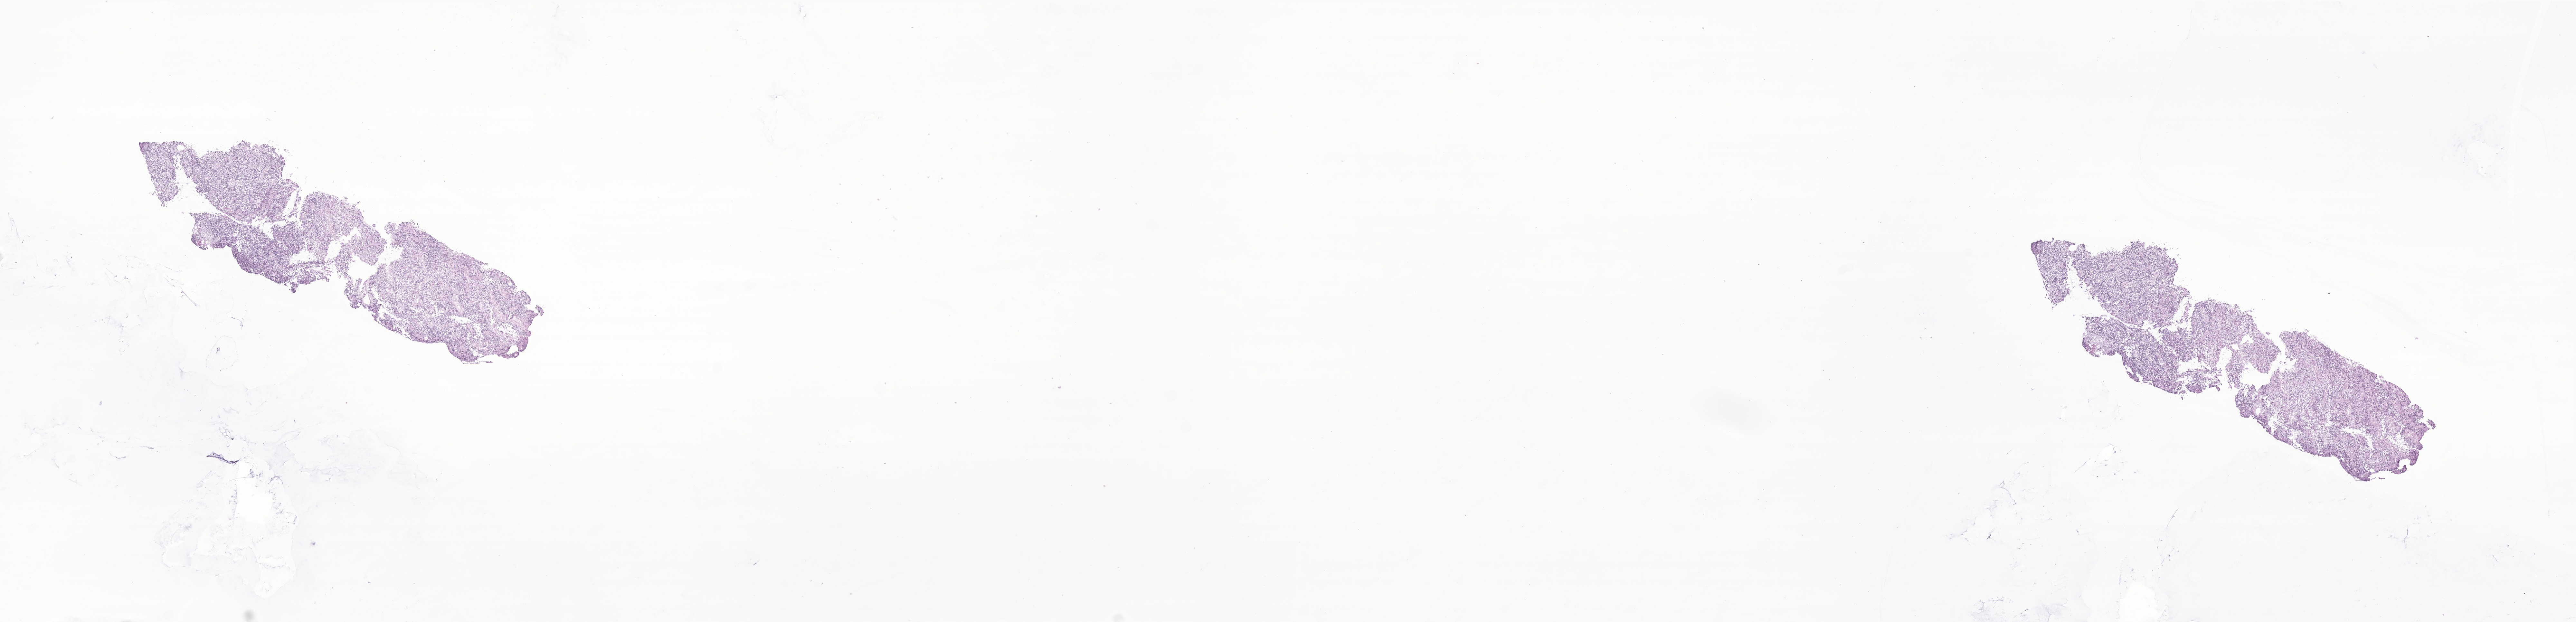
Whole-slide image, hematoxylin and eosin (H&E) stain of tumor tissue from the cerebral ventricle, shown as a low-resolution overview of the whole scanned area (about 33.7 x 8.1 mm). Cryosection (OCT / tissue freezing medium). Female patient, age 427 days (about 1.2 years).
* diagnosis: Ependymoma, NOS